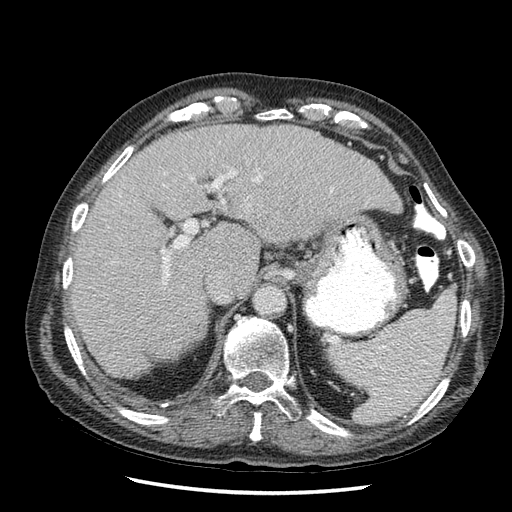
Contrast-enhanced abdominal CT (liver protocol), one axial slice; reconstruction kernel STANDARD; 120 kVp; soft-tissue window (W 400 / L 40 HU); 2.5 mm slice thickness; 512 × 512 image matrix, field of view 360 × 360 mm. From the clinical record (not read from this slice): diagnosis: hepatocellular carcinoma (patient treated with transarterial chemoembolisation; whether this scan precedes or follows treatment is not stated here); TNM stage (as recorded): Stage-I; Child-Pugh class: A; tumour nodularity: uninodular.
Outlined on this slice (semi-automatic segmentation, software-assisted and operator-edited):
- liver parenchyma outside the tumour (the mass and vessels are separate outlines, so this box may not span the whole liver): box from (x=70, y=124) to (x=400, y=378) px
- liver vessels: (x=106, y=168)–(x=251, y=290)